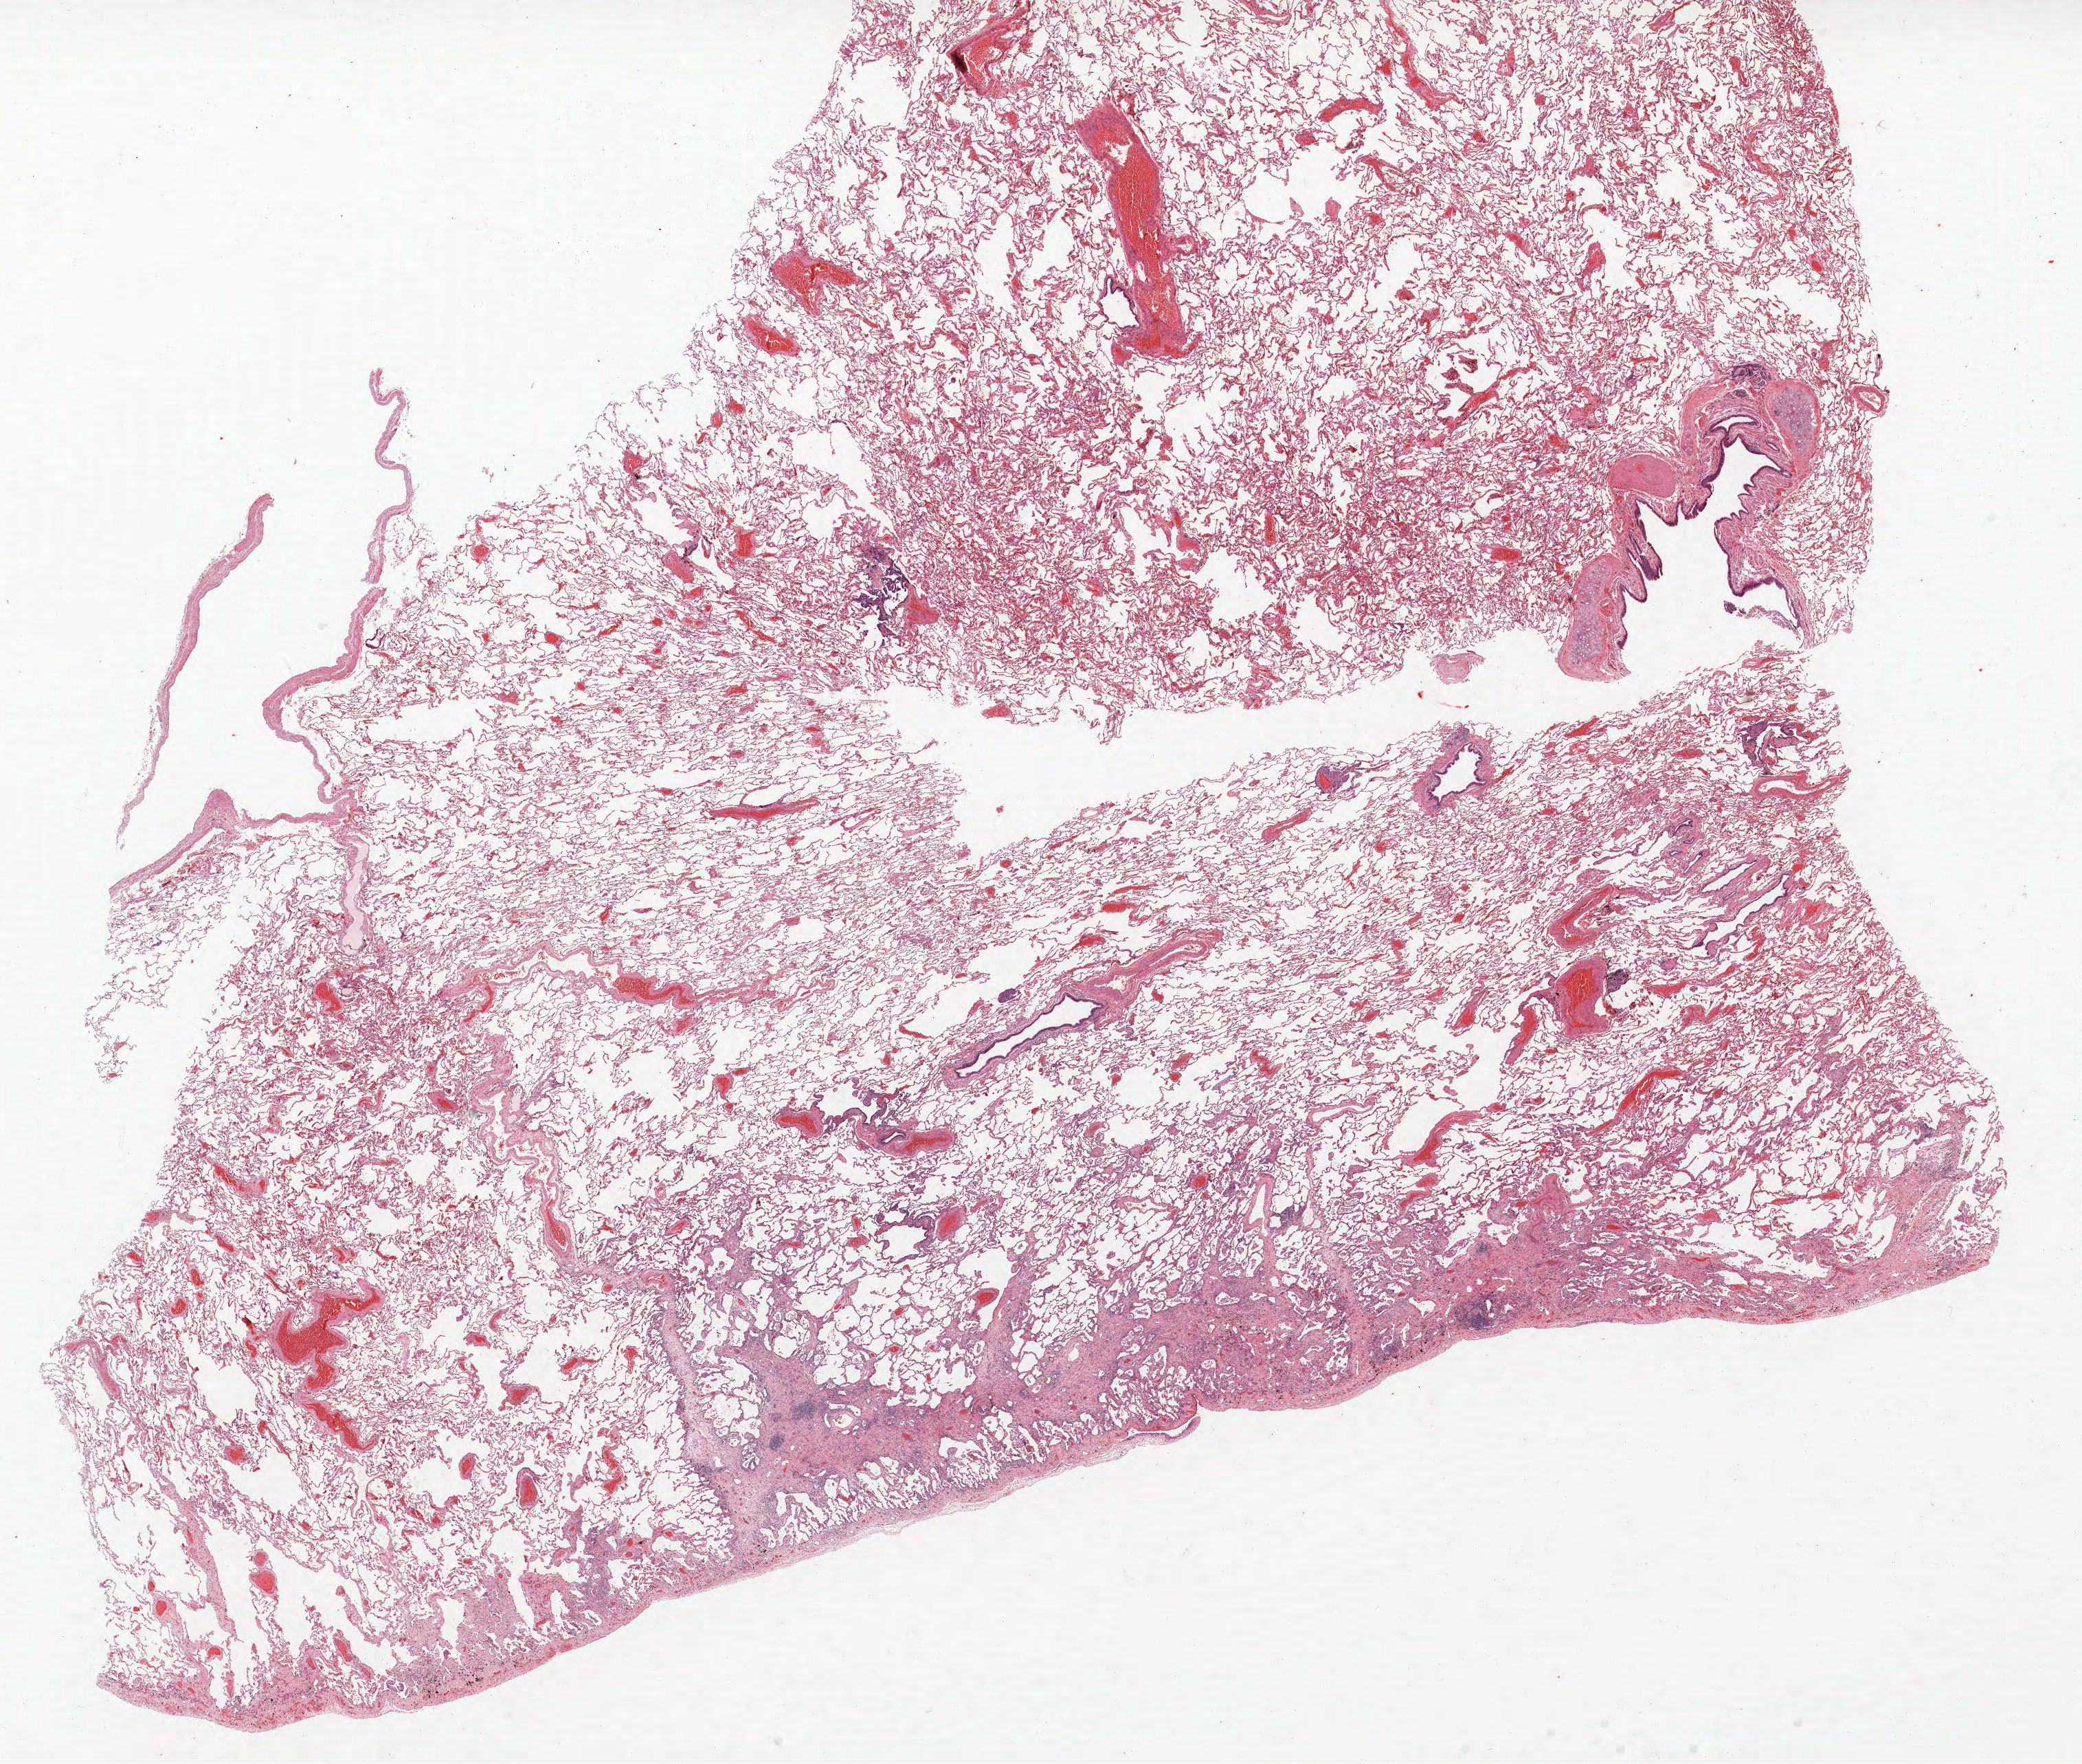
Hematoxylin and eosin (H&E) stained whole-slide image — shown as a low-resolution overview of the whole scanned area (about 24.2 x 20.5 mm, slide scanned at 40x); formalin-fixed paraffin-embedded (FFPE) section; lung tissue. Male patient, aged 61 at enrolment. Former smoker at enrolment. Grade: poorly differentiated (G3).
- stage (AJCC 6th edition): IB
- tumour size (pathology): 35 mm
- primary tumour location (clinical record): left upper lobe
- participant's lung-cancer diagnosis: Adenocarcinoma, NOS (ICD-O-3 8140/3)